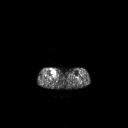
FDG PET of an extremity soft-tissue mass (from a PET/CT study), one axial slice. Position 136 of 267 along the scan axis. 3.27 mm slice thickness. 128 × 128 image matrix, field of view 700 × 700 mm. Patient: female, 65 years. Case-level facts recorded for this patient, not image findings: histological type: undifferentiated – high grade; grade: high; site of the primary tumour: right thigh.
Structures marked on this image (expert contour drawn on MRI and transferred to this co-registered scan by the dataset authors):
- gross tumour volume (mass): bounding box (x1, y1, x2, y2) in pixels: (51, 69, 56, 75)